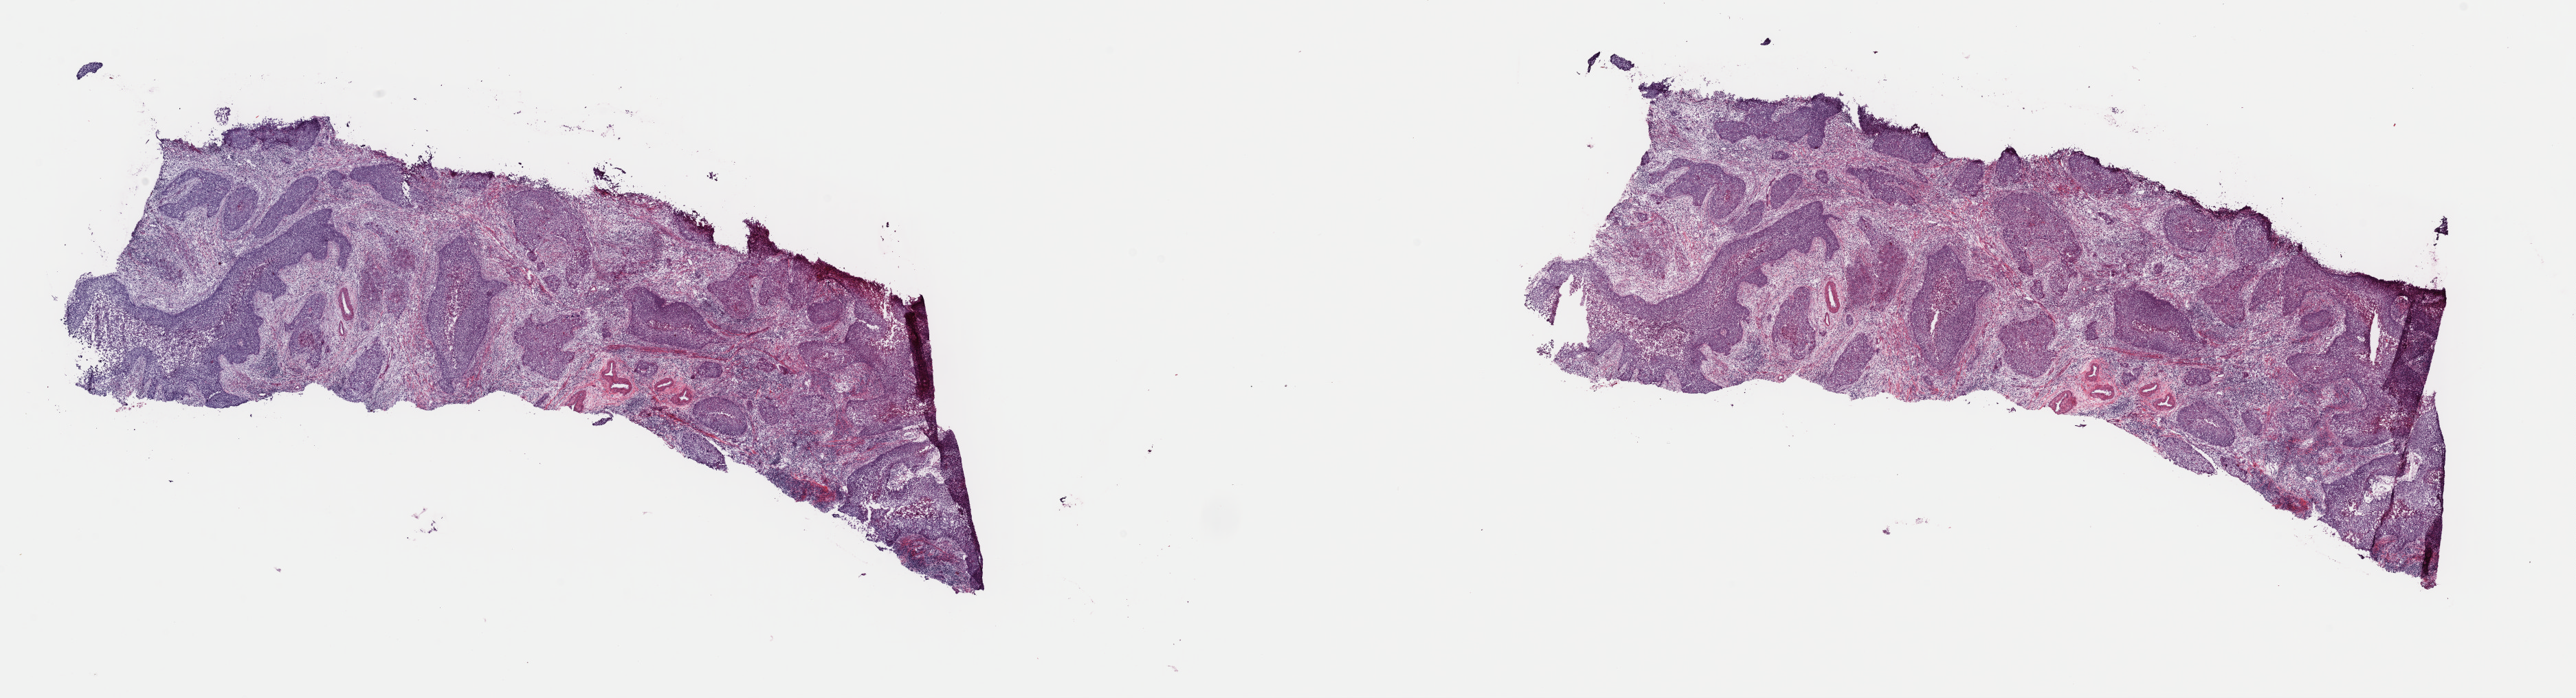
Hematoxylin and eosin (H&E) stained whole-slide image — low-resolution overview of the scanned area, about 29.6 x 8.0 mm (acquisition: 40x scan); frozen section from the top of the tissue portion; primary tumour sample from the cervix. Female patient; age at initial diagnosis 54 years. Composition of this section per pathologist review: tumour cells 60%, tumour nuclei 60%.
Diagnosis: Squamous cell carcinoma, NOS (cervix uteri).